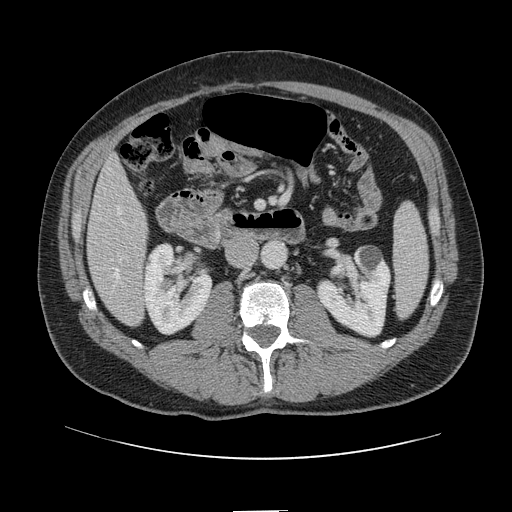
Contrast-enhanced abdominal CT, one axial slice. Position 35 of 161 along the scan axis. 120 kVp. Intravenous contrast given. Soft-tissue window (W 400 / L 40 HU). 512 × 512 image matrix. Male patient, age 66 years. From the clinical record (not read from this slice): diagnosis: colorectal cancer liver metastases, imaged before liver resection; multiple liver metastases: no; largest metastasis: 3.5 cm; disease in both lobes: no.
Annotated regions visible in this slice (expert manual segmentation):
- hepatic veins: bounding box <116,208,122,280> (left, top, right, bottom; pixels)
- liver: <88,159,148,325>
- planned liver remnant (the part of the liver to remain after resection): <87,159,146,265>